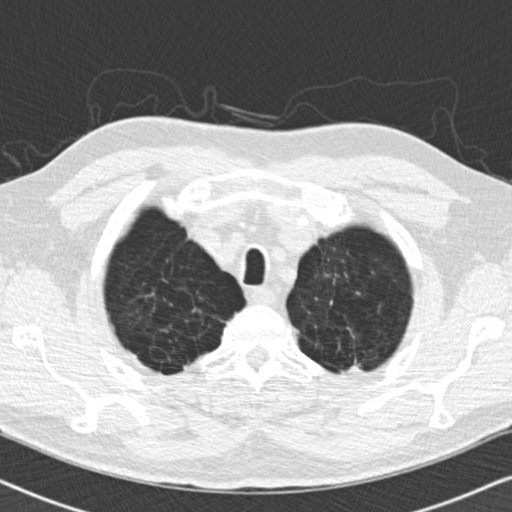
Low-dose screening chest CT, one axial slice. Slice 156 of 175 in the series (ordered by position). Reconstruction kernel B30f. Lung window (W 1500 / L -600 HU). 512 × 512 image matrix.
Outlined on this slice (outlined manually by an expert reader):
- lesion 1 (tumor, upper lobe of left lung): bounding box <347,359,363,372> (left, top, right, bottom; pixels)